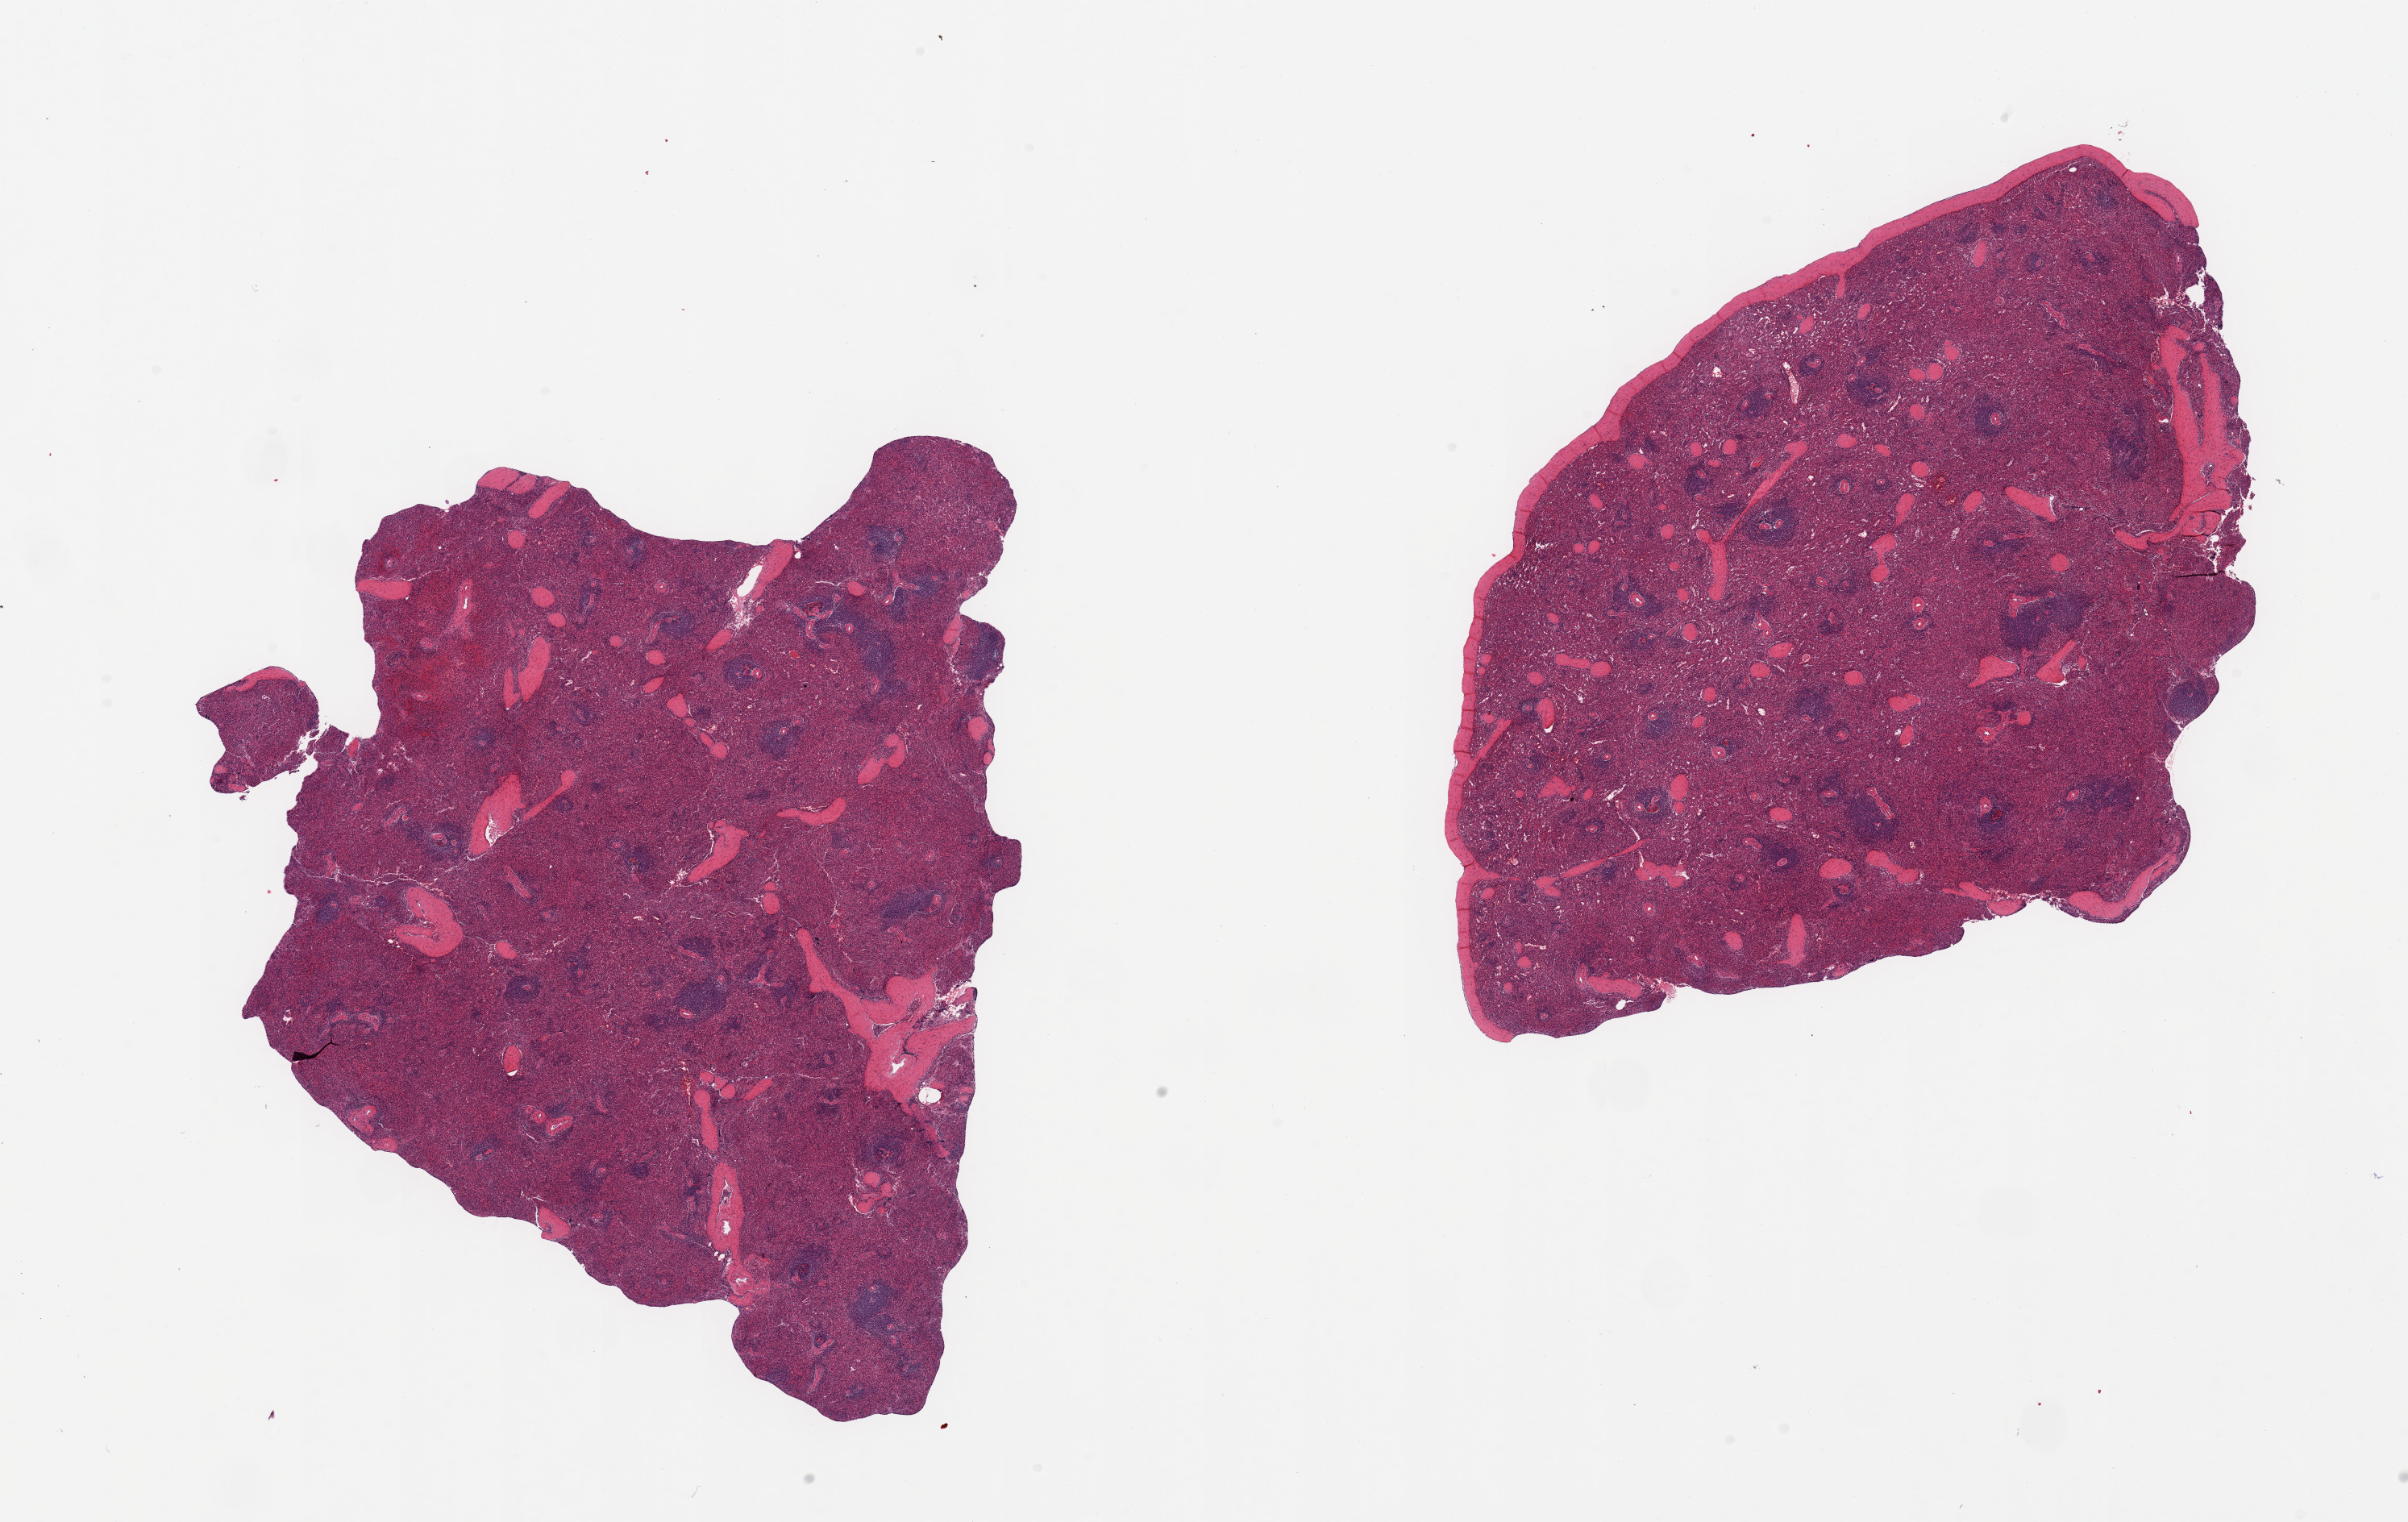
Digitized haematoxylin and eosin-stained section, brightfield, shown as a low-resolution overview of the whole scanned area (about 23.6 x 14.9 mm), PAXgene-fixed, paraffin-embedded tissue, sampled site (target tissue): spleen, donor tissue sample. Male donor.
Reviewer comment on this tissue sample: 2 pieces; 1 piece includes capsule (target is 5mm below capsule).